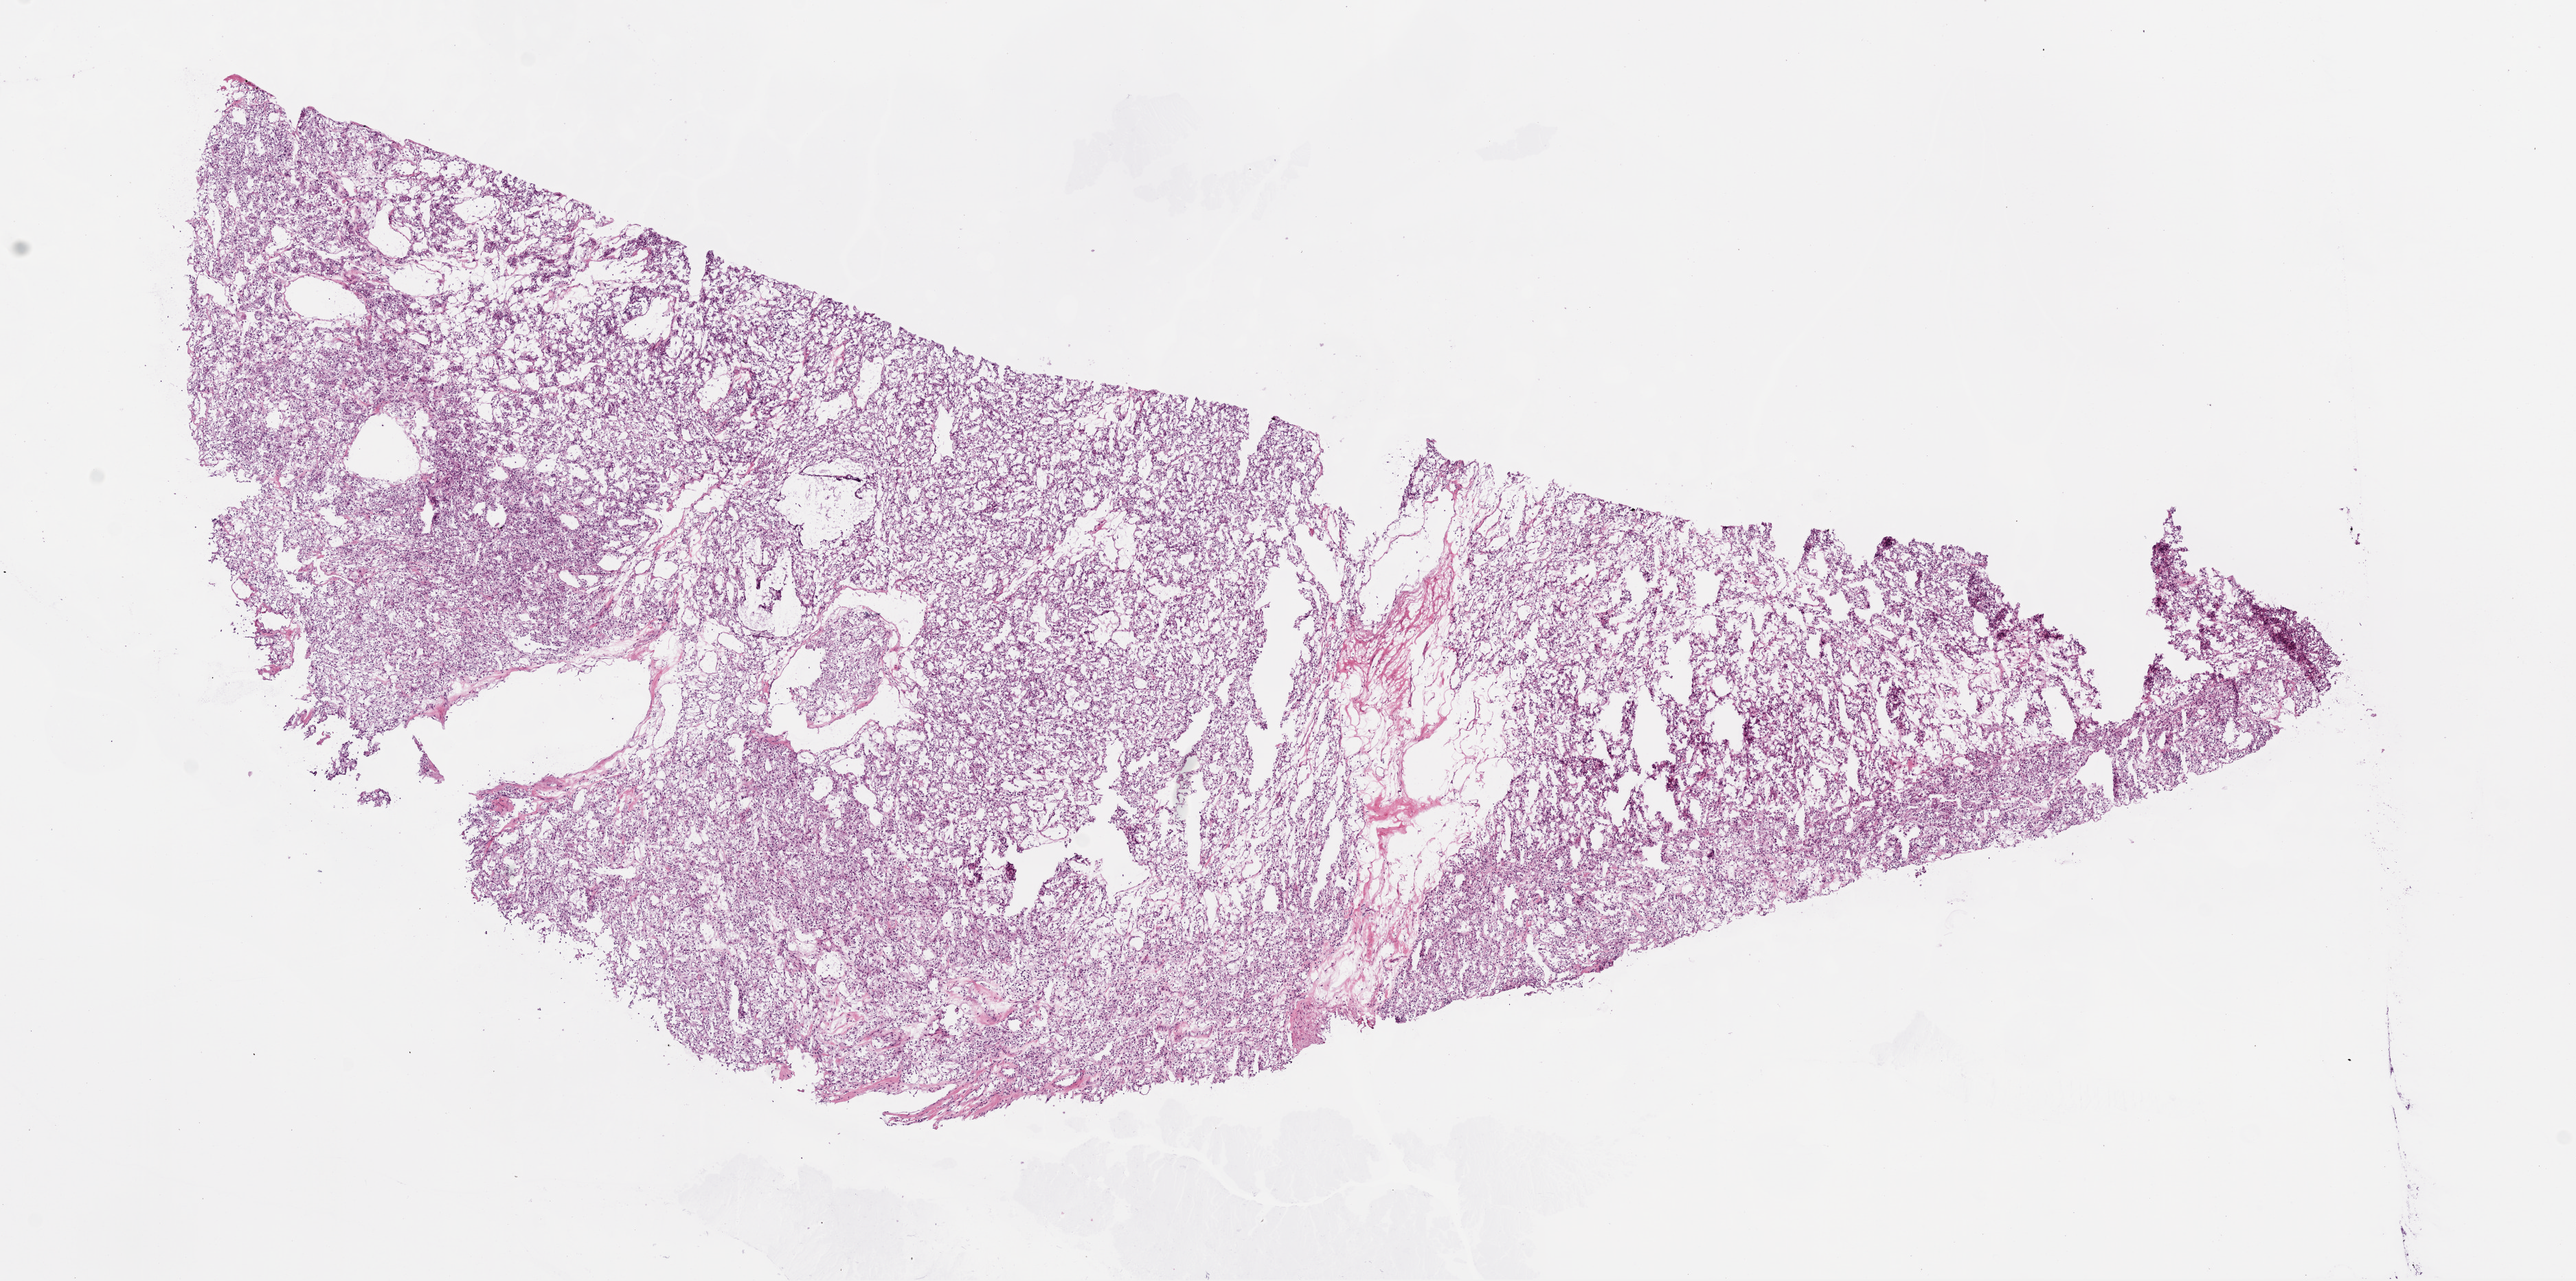
Digitized Hematoxylin and eosin (H&E) stained tissue section (whole slide), a low-resolution overview of the entire scanned area, about 15.0 x 7.5 mm; frozen section from the top of the tissue portion; kidney, primary tumour sample. Patient: female, age at initial diagnosis 75 years. Histologic grade: G3 (poorly differentiated). Slide review estimates, as recorded: tumour cells 90%, tumour nuclei 85%, normal cells 0%, stromal cells 10%, necrosis 0%.
AJCC pathologic stage: III (6th edition). Histologic diagnosis: Clear cell adenocarcinoma, NOS. TNM: T3b N0 M0.